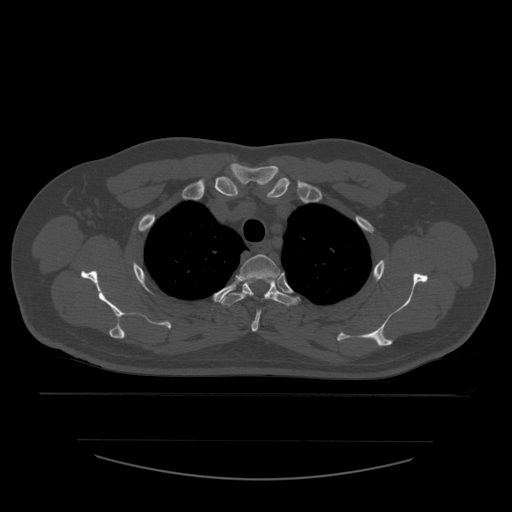
CT including the spine, one axial slice. Slice 441 of 532 in the series (ordered by position). 120 kVp. Bone window (W 1800 / L 400 HU). 1.25 mm slice thickness. 512 × 512 image matrix. Patient age 44 years. From the clinical record (not read from this slice): primary cancer: soft tissue sarcoma.
Outlined on this slice (semi-automatically segmented with operator editing):
- T2 vertebra: box from (x=240, y=255) to (x=281, y=332) px
- T3 vertebra: (x=218, y=277)–(x=299, y=307)